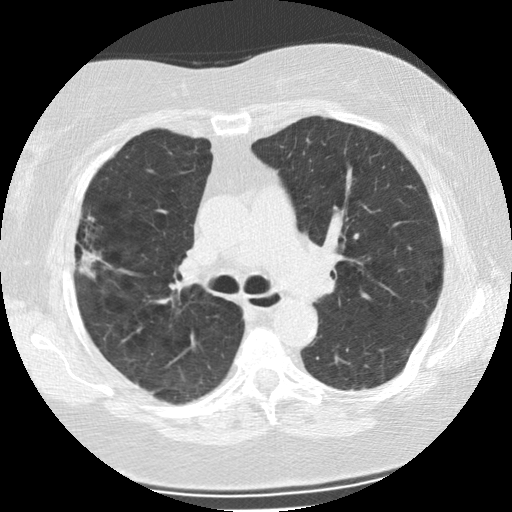
Axial slice from a low-dose chest CT screening exam. Second annual screen. Lung window (W 1500 / L -600 HU). 2.5 mm slice thickness. 512 × 512 image matrix, field of view 320 × 320 mm. Female participant, aged 73 years at enrolment. Former smoker at enrolment.
- Lesion marked by an expert reader, box from (x=54, y=218) to (x=112, y=288) px.
- The screening reader recorded 2 non-calcified nodules or masses ≥4 mm on this exam; which of them this box marks is not recorded.
- Official screen result: positive, change unspecified: nodule(s) >= 4 mm or enlarging nodule(s), mass(es), or other non-specific abnormalities suspicious for lung cancer.
- Later outcome: lung cancer diagnosed 47 days after this screen — bronchiolo-alveolar adenocarcinoma, NOS, right upper lobe, moderately differentiated (G2), stage IIIB (AJCC 6th edition), 21 mm at pathology.